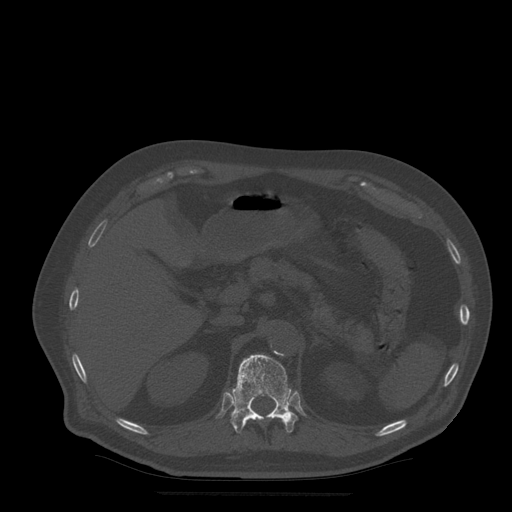
CT including the spine, one axial slice; position 224 of 522 along the scan axis; bone window (W 1800 / L 400 HU); 1.25 mm slice thickness; 512 × 512 image matrix, field of view 420 × 420 mm. Patient age 72 years. Case-level facts recorded for this patient, not image findings: primary cancer: prostate.
Structures marked on this image (semi-automatically segmented with operator editing):
- T12 vertebra: box from (x=231, y=355) to (x=298, y=433) px